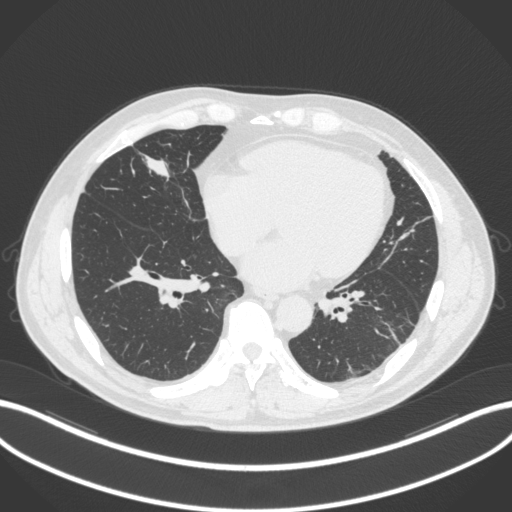
Chest CT, one axial slice; slice 99 of 399 in the series (ordered by position); reconstruction kernel B31f; 120 kVp; lung window (W 1500 / L -600 HU); 512 × 512 image matrix, field of view 400 × 400 mm. Male patient, age 59 years. From the clinical record (not read from this slice): clinical TNM (as recorded): T2a N1 M0.
Annotated regions visible in this slice (bounding box drawn by a radiologist):
- lung tumour (recorded histology: adenocarcinoma): bounding box <136,147,178,194> (left, top, right, bottom; pixels)